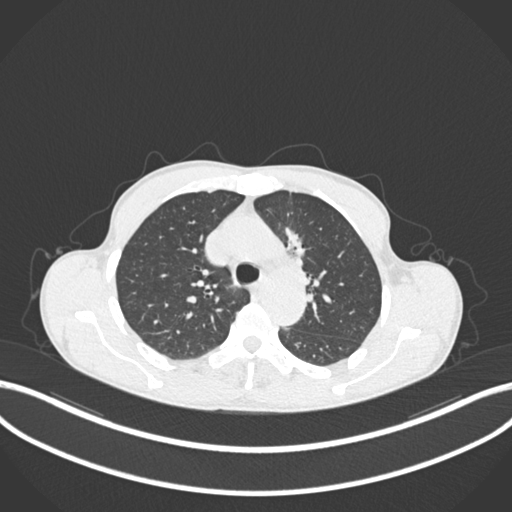
Chest CT, one axial slice. Reconstruction kernel B30f. Lung window (W 1500 / L -600 HU). 1 mm slice thickness. 512 × 512 image matrix, field of view 400 × 400 mm. Male patient, age 58 years. From the clinical record (not read from this slice): clinical TNM (as recorded): T1c N1 M0.
Outlined on this slice (rectangle marked by the reading radiologist):
- lung tumour (recorded histology: adenocarcinoma): bounding box (x1, y1, x2, y2) in pixels: (282, 218, 311, 271)